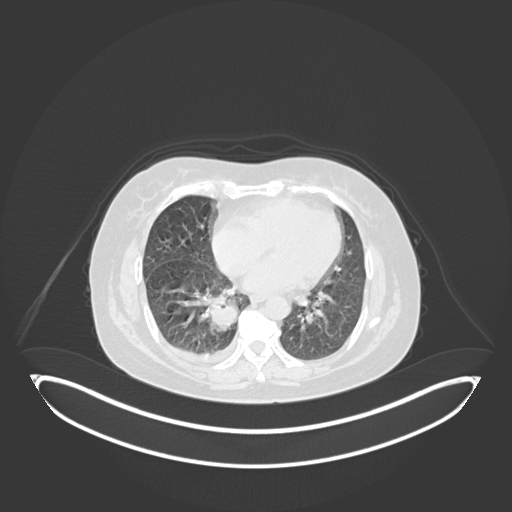
Chest CT, one axial slice. Position 60 of 231 along the scan axis. Lung window (W 1500 / L -600 HU). 512 × 512 image matrix. Patient: female, 56 years. Case-level facts recorded for this patient, not image findings: clinical TNM (as recorded): T2b N1 M0.
Outlined on this slice (bounding box drawn by a radiologist):
- lung tumour (recorded histology: small cell carcinoma): bounding box (x1, y1, x2, y2) in pixels: (208, 297, 244, 339)